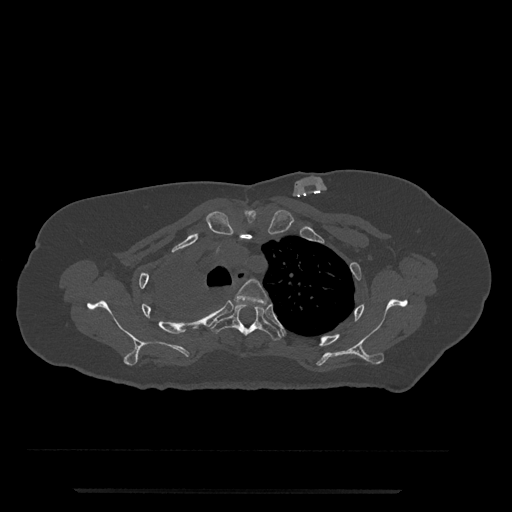
CT including the spine, one axial slice. Slice 604 of 797 in the series (ordered by position). Reconstruction kernel Br40s/3. 120 kVp. Bone window (W 1800 / L 400 HU). 512 × 512 image matrix, field of view 440 × 440 mm. Female patient, age 51 years. Case-level facts recorded for this patient, not image findings: primary cancer: neuro; vertebrae with lytic lesions (as recorded): T8.
Annotated regions visible in this slice (semi-automatic segmentation, software-assisted and operator-edited):
- T3 vertebra: bounding box <234,278,269,305> (left, top, right, bottom; pixels)
- T4 vertebra: <210,304,282,341>